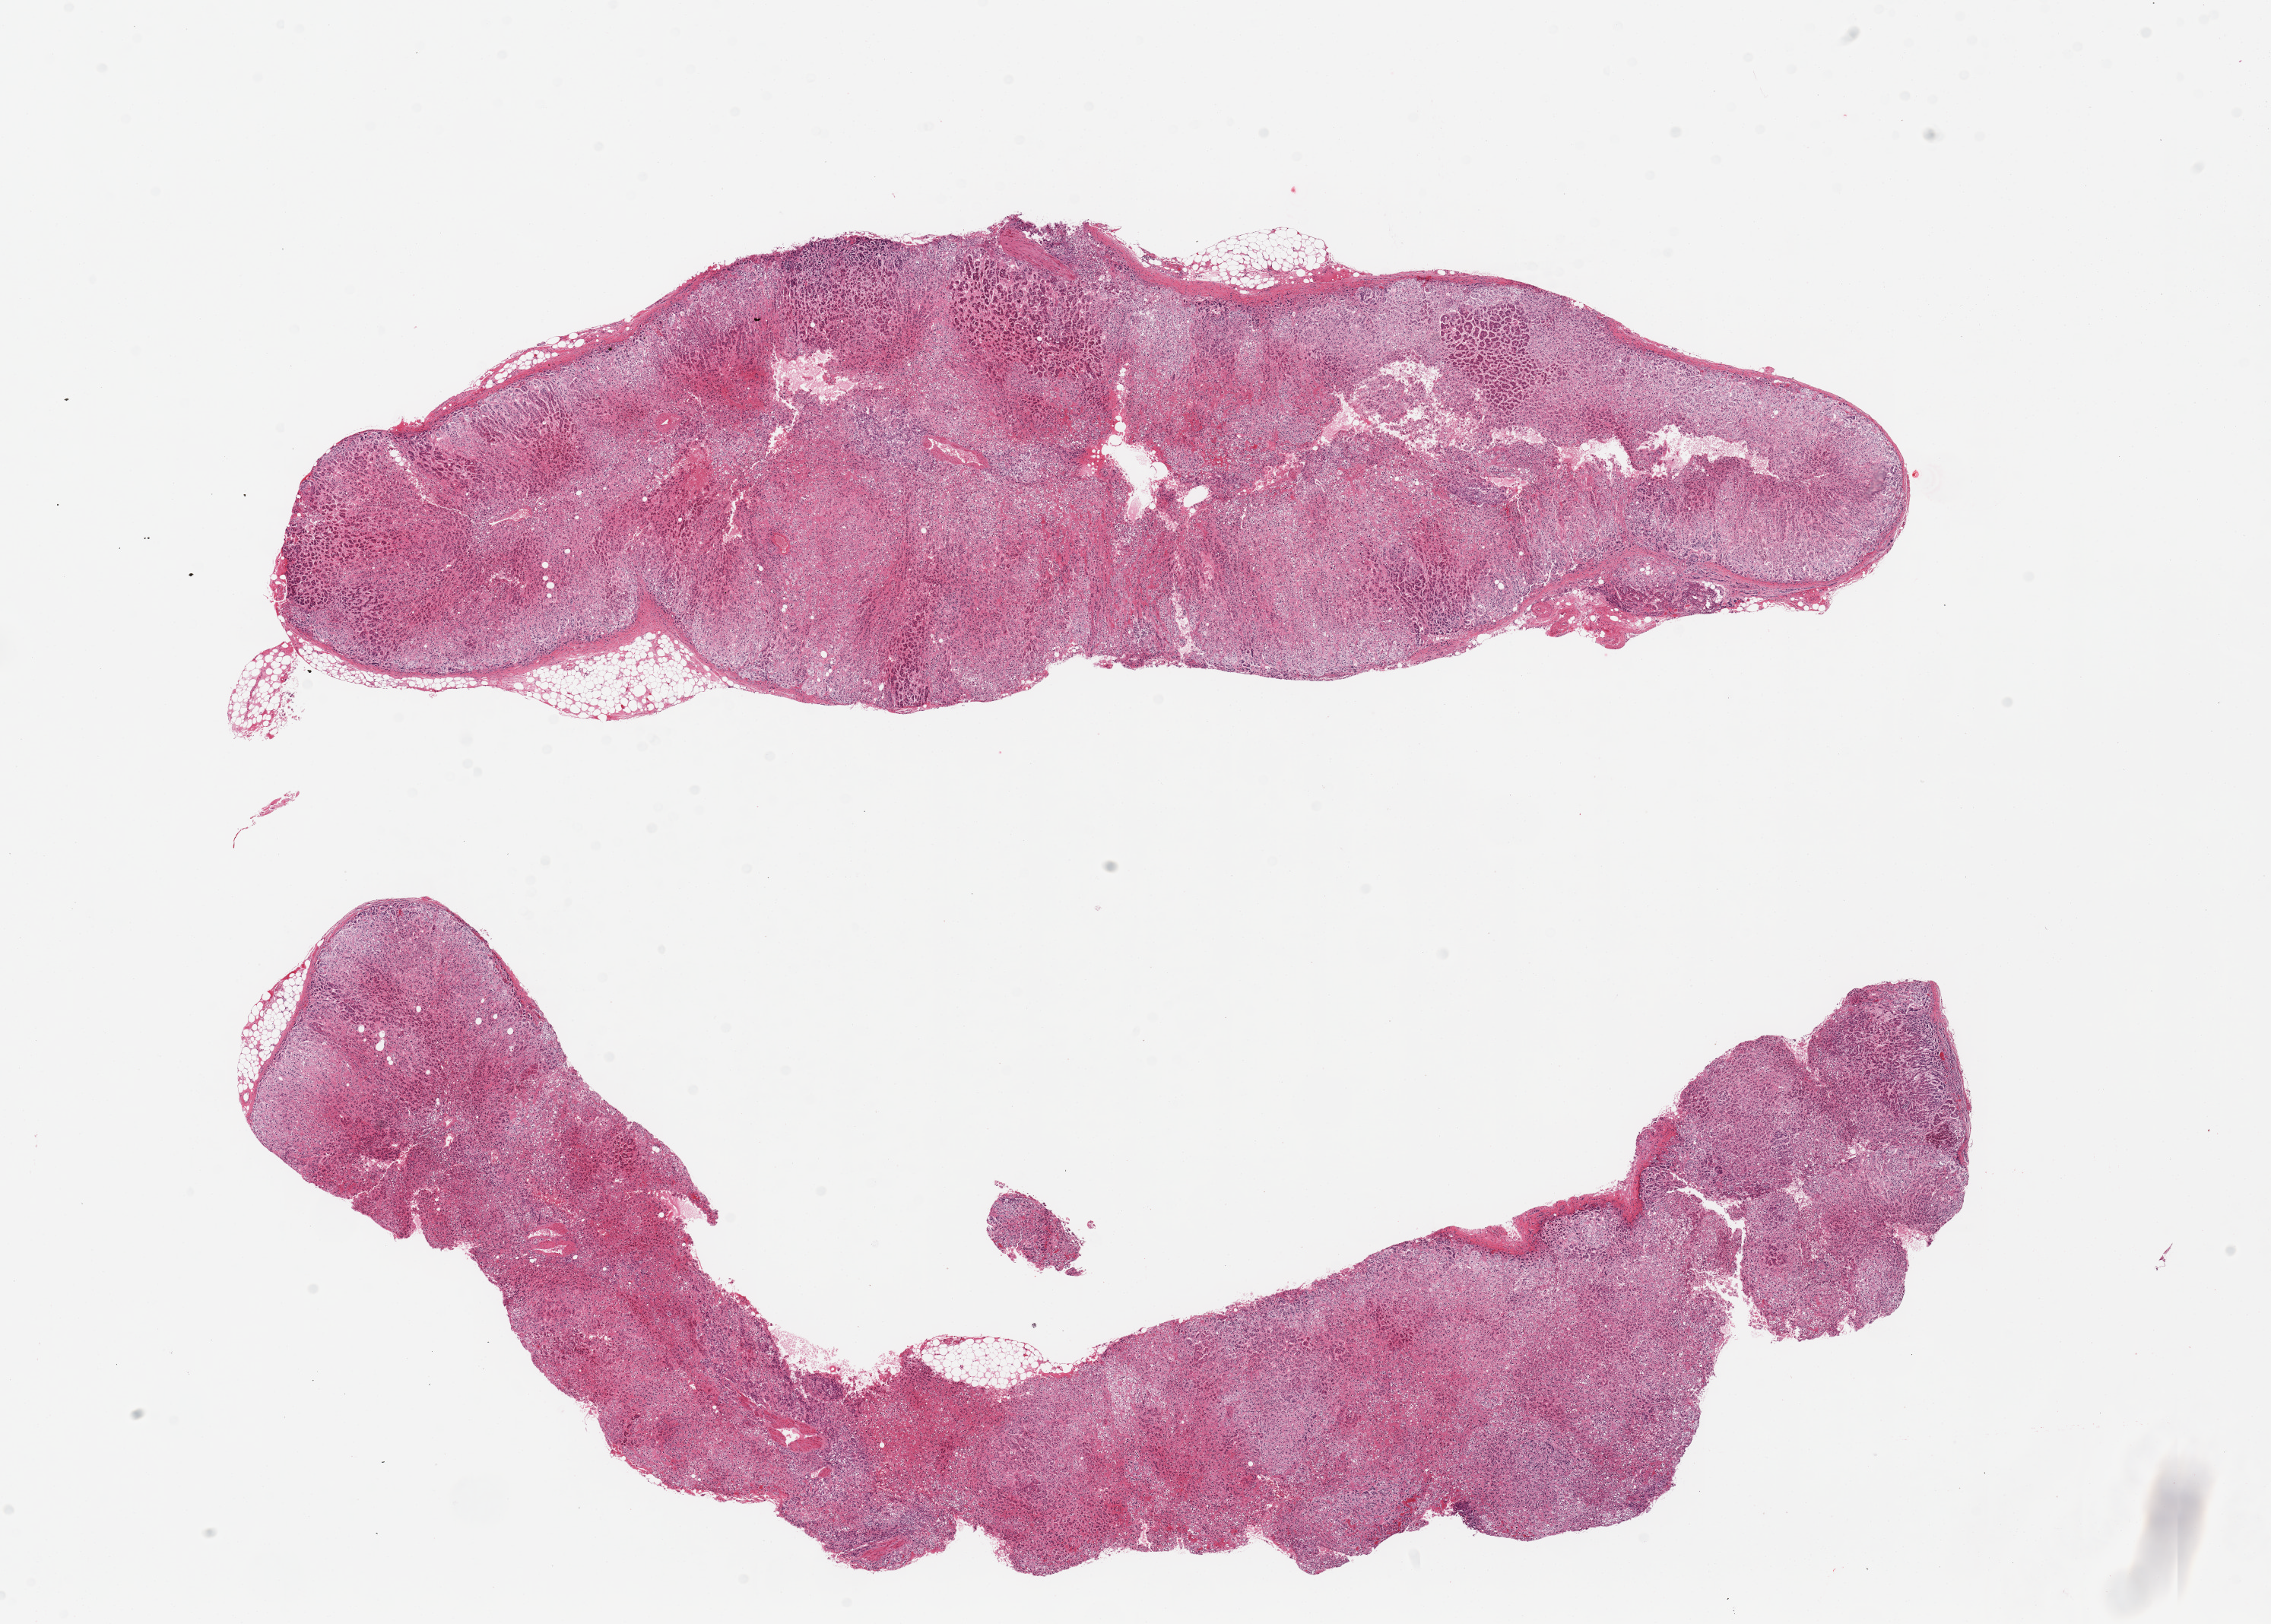
H&E whole-slide image, brightfield, shown as a low-resolution overview of the whole scanned area (about 23.6 x 16.9 mm). PAXgene-fixed paraffin-embedded (PFPE) section. Section of adrenal gland (target tissue). Tissue donor sample.
Pathologist's review note for this sample: 2 pieces; well dissected.